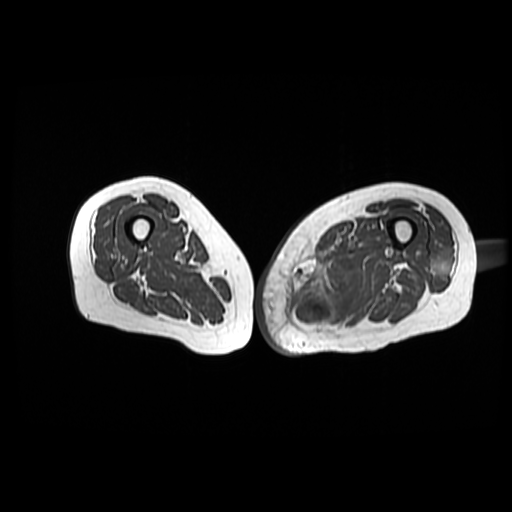
MRI of an extremity soft-tissue mass, one axial slice; slice 37 of 42 in the series (ordered by position); 6 mm slice thickness; 512 × 512 image matrix, field of view 420 × 420 mm. Female patient. From the clinical record (not read from this slice): histological type: pleomorphic leiomyosarcoma; grade: high; site of the primary tumour: left thigh.
Structures marked on this image (expert manual segmentation):
- gross tumour volume including surrounding oedema: box from (x=287, y=250) to (x=361, y=335) px
- gross tumour volume (mass): (x=309, y=293)–(x=337, y=320)